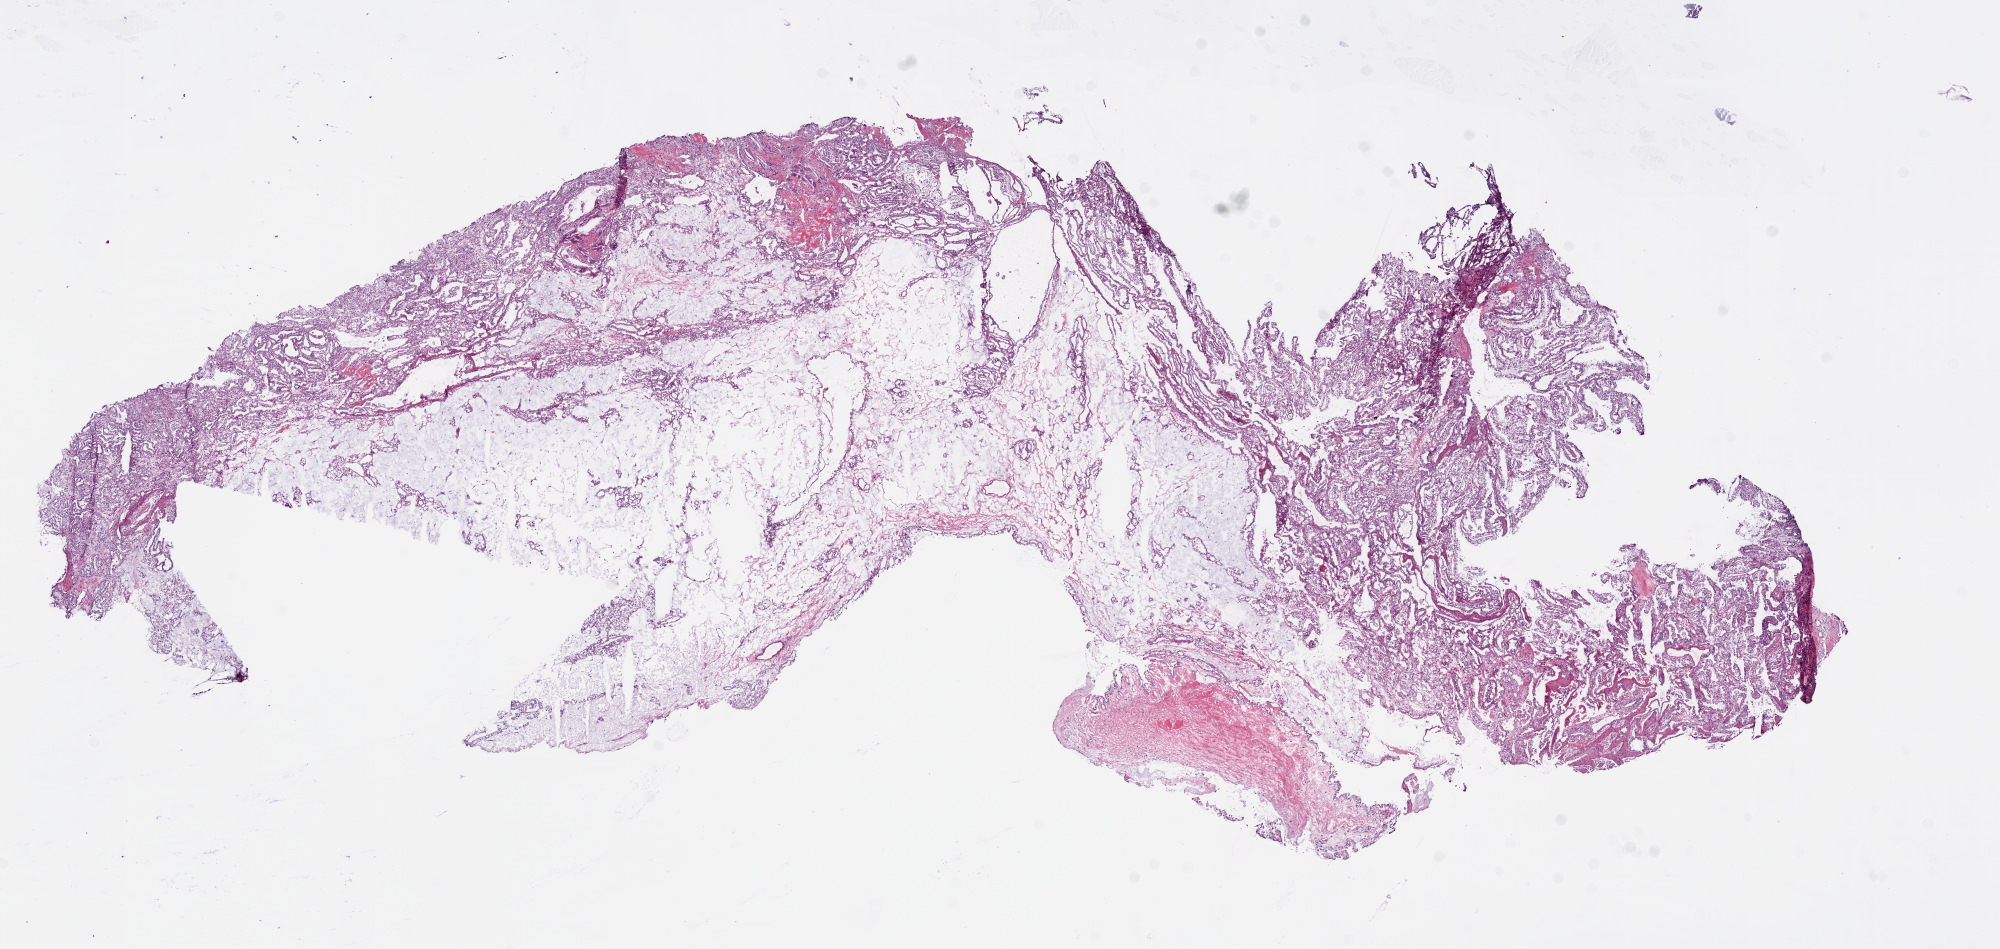
H&E whole-slide image, whole scanned area (about 16.0 x 7.6 mm, acquisition: 20x scan) shown as a low-resolution overview, frozen section, primary tumour sample from the kidney. Male patient; age at initial diagnosis 69 years. Histologic grade: G2 (moderately differentiated). Pathologist review of this section (percent, as recorded): tumour cells 95%, tumour nuclei 85%, stromal cells 5%, necrosis 0%. Infiltration values recorded for this section: lymphocyte infiltration 1%.
Diagnosis: Clear cell adenocarcinoma, NOS. Laterality: left. AJCC pathologic stage: I.